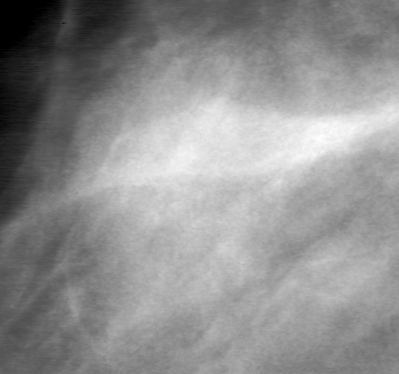
Region of interest cut from a scanned film mammogram (one marked finding), right breast, MLO view, BI-RADS breast density category 2 (scale 1–4).
Finding: mass, shape lobulated, margins obscured; BI-RADS assessment category 0; pathology result (as recorded, not read from the image): benign.